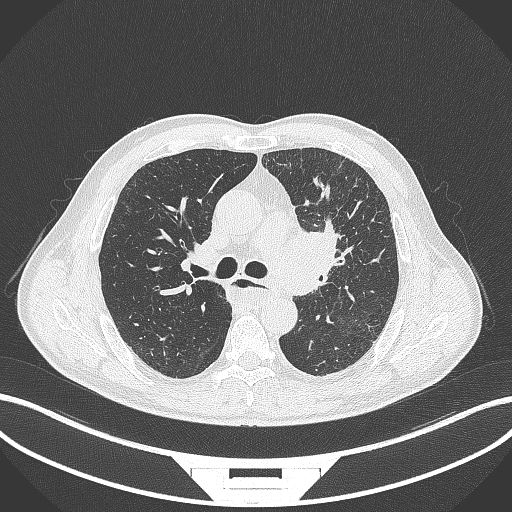
Chest CT, one axial slice; slice 242 of 411 in the series (ordered by position); lung window (W 1500 / L -600 HU); 512 × 512 image matrix, field of view 400 × 400 mm. Patient: male, 57 years. From the clinical record (not read from this slice): clinical TNM (as recorded): T2a N1 M0.
Structures marked on this image (bounding box drawn by a radiologist):
- lung tumour (recorded histology: squamous cell carcinoma): bounding box [x1, y1, x2, y2] px = [271, 221, 358, 299]